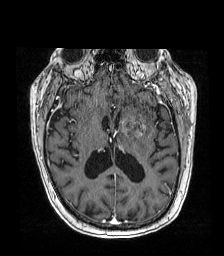
Brain MRI from a brain-tumour surgery series, one axial slice. Slice 82 of 192 in the series (ordered by position). T1-weighted post-contrast. 224 × 256 image matrix, field of view 219 × 250 mm. Case-level facts recorded for this patient, not image findings: histopathology: Metastatic carcinoma from lung primary; tumour location: Left Frontal Caudate.
Structures marked on this image (manually delineated by an expert):
- tumour: bounding box <117,115,148,138> (left, top, right, bottom; pixels)